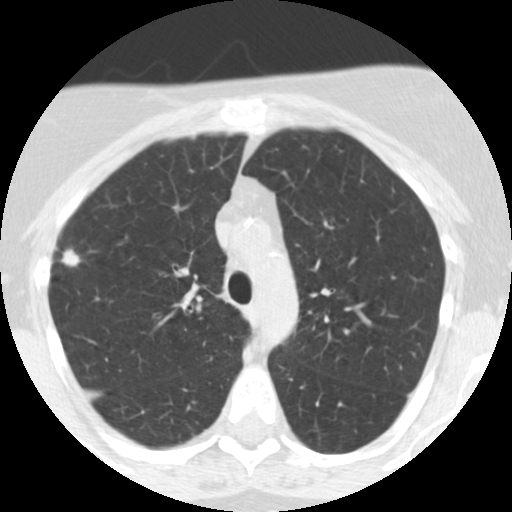
Axial slice from a low-dose chest CT screening exam; third annual screen; lung window (W 1500 / L -600 HU); 2.5 mm slice thickness; slice 180 of 248 in the series; 512 × 512 image matrix. Female participant, aged 55 years at enrolment. Current smoker at enrolment.
Lesion marked by an expert reader, bounding box [x1, y1, x2, y2] px = [47, 242, 91, 282]. The exam's reader record, not a measurement of the box and not confirmed to be the same lesion: non-calcified nodule or mass ≥4 mm, right upper lobe, 10 × 10 mm, poorly defined margins, soft tissue attenuation, pre-existing on the prior screen: yes; interval growth: yes. Official screen result: positive, other. Lung cancer was diagnosed 145 days after this screen: bronchiolo-alveolar adenocarcinoma, NOS, right upper lobe, moderately differentiated (G2), stage IIA (AJCC 6th edition), 13 mm at pathology.